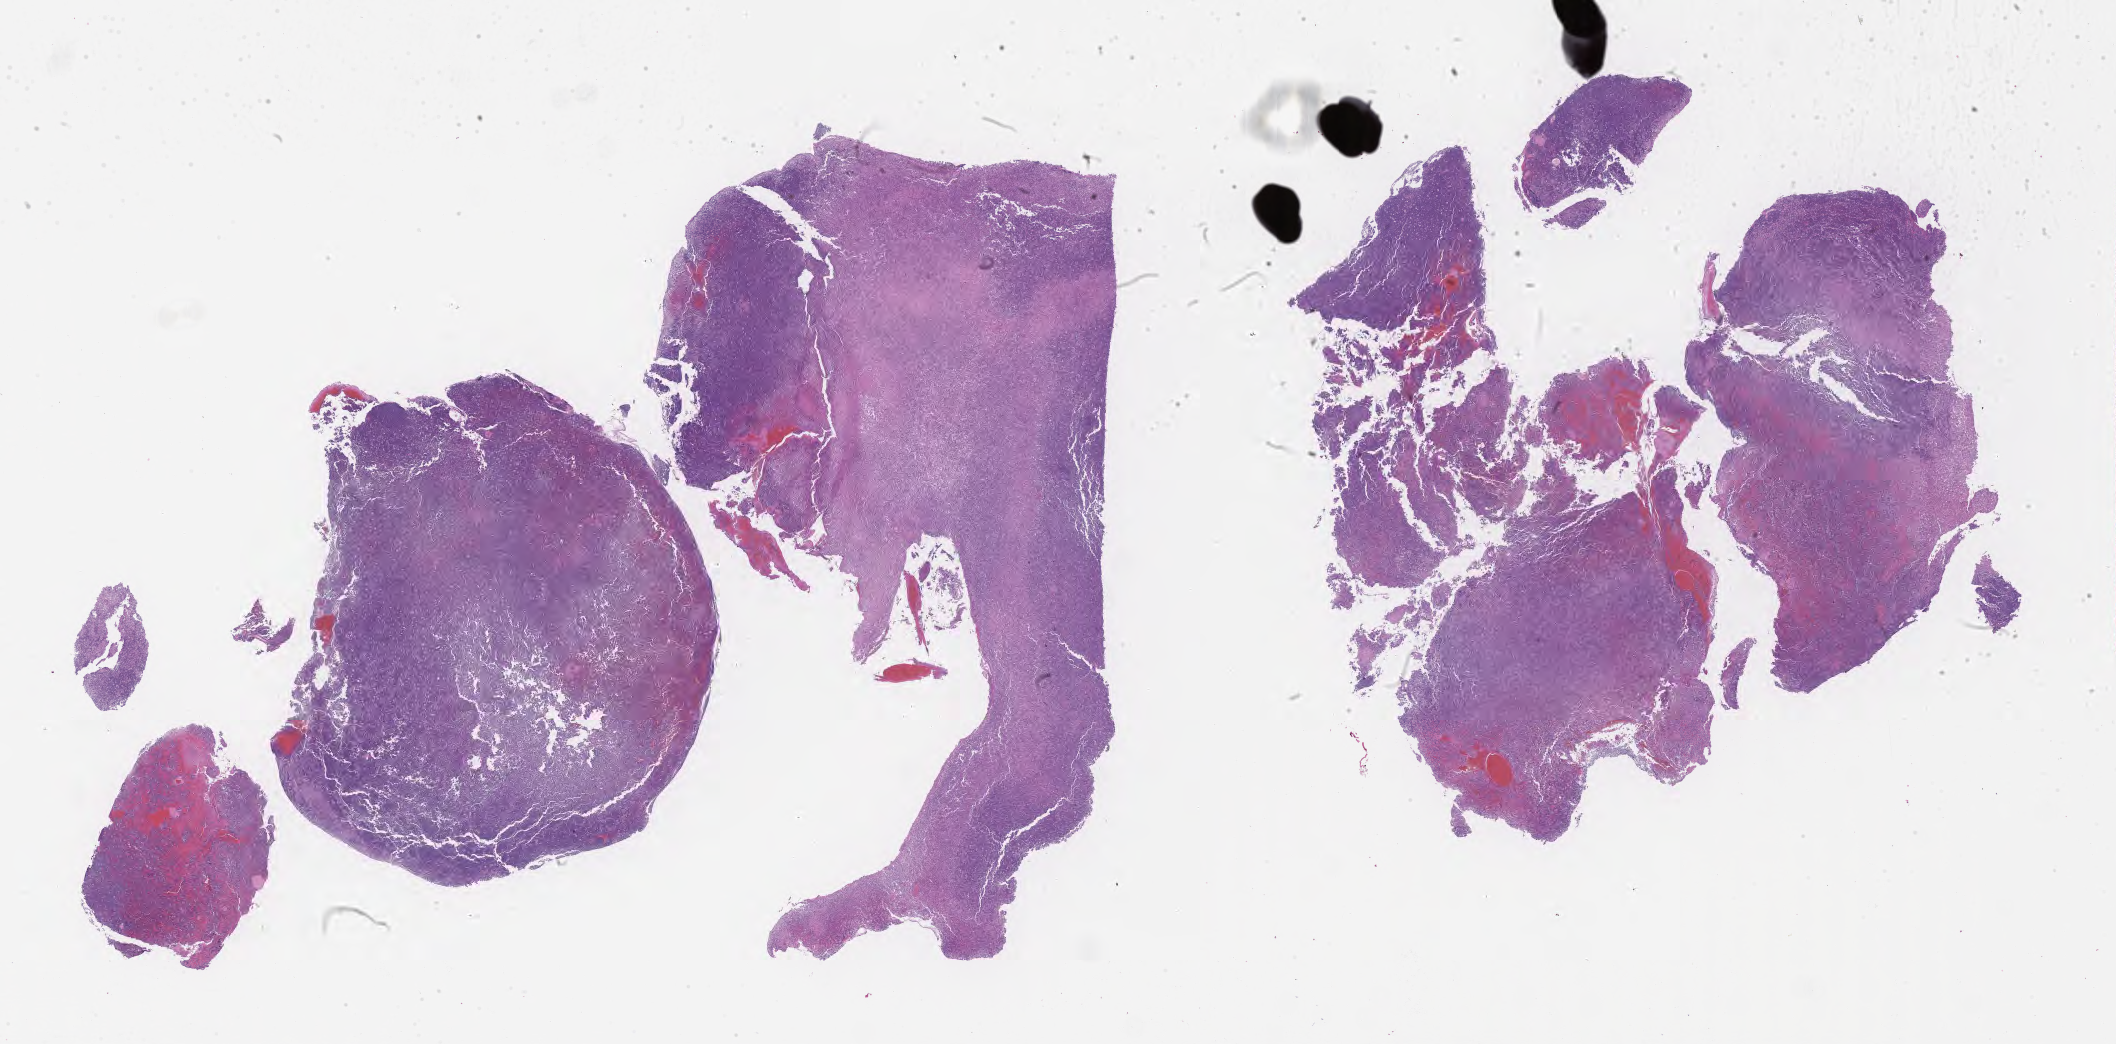
Hematoxylin and eosin (H&E) whole-slide image, shown as a low-resolution overview of the whole scanned area (about 34.2 x 16.9 mm). Specimen: tumor tissue. Male, age 4 years at initial diagnosis.
Diagnosis: Burkitt lymphoma, NOS.